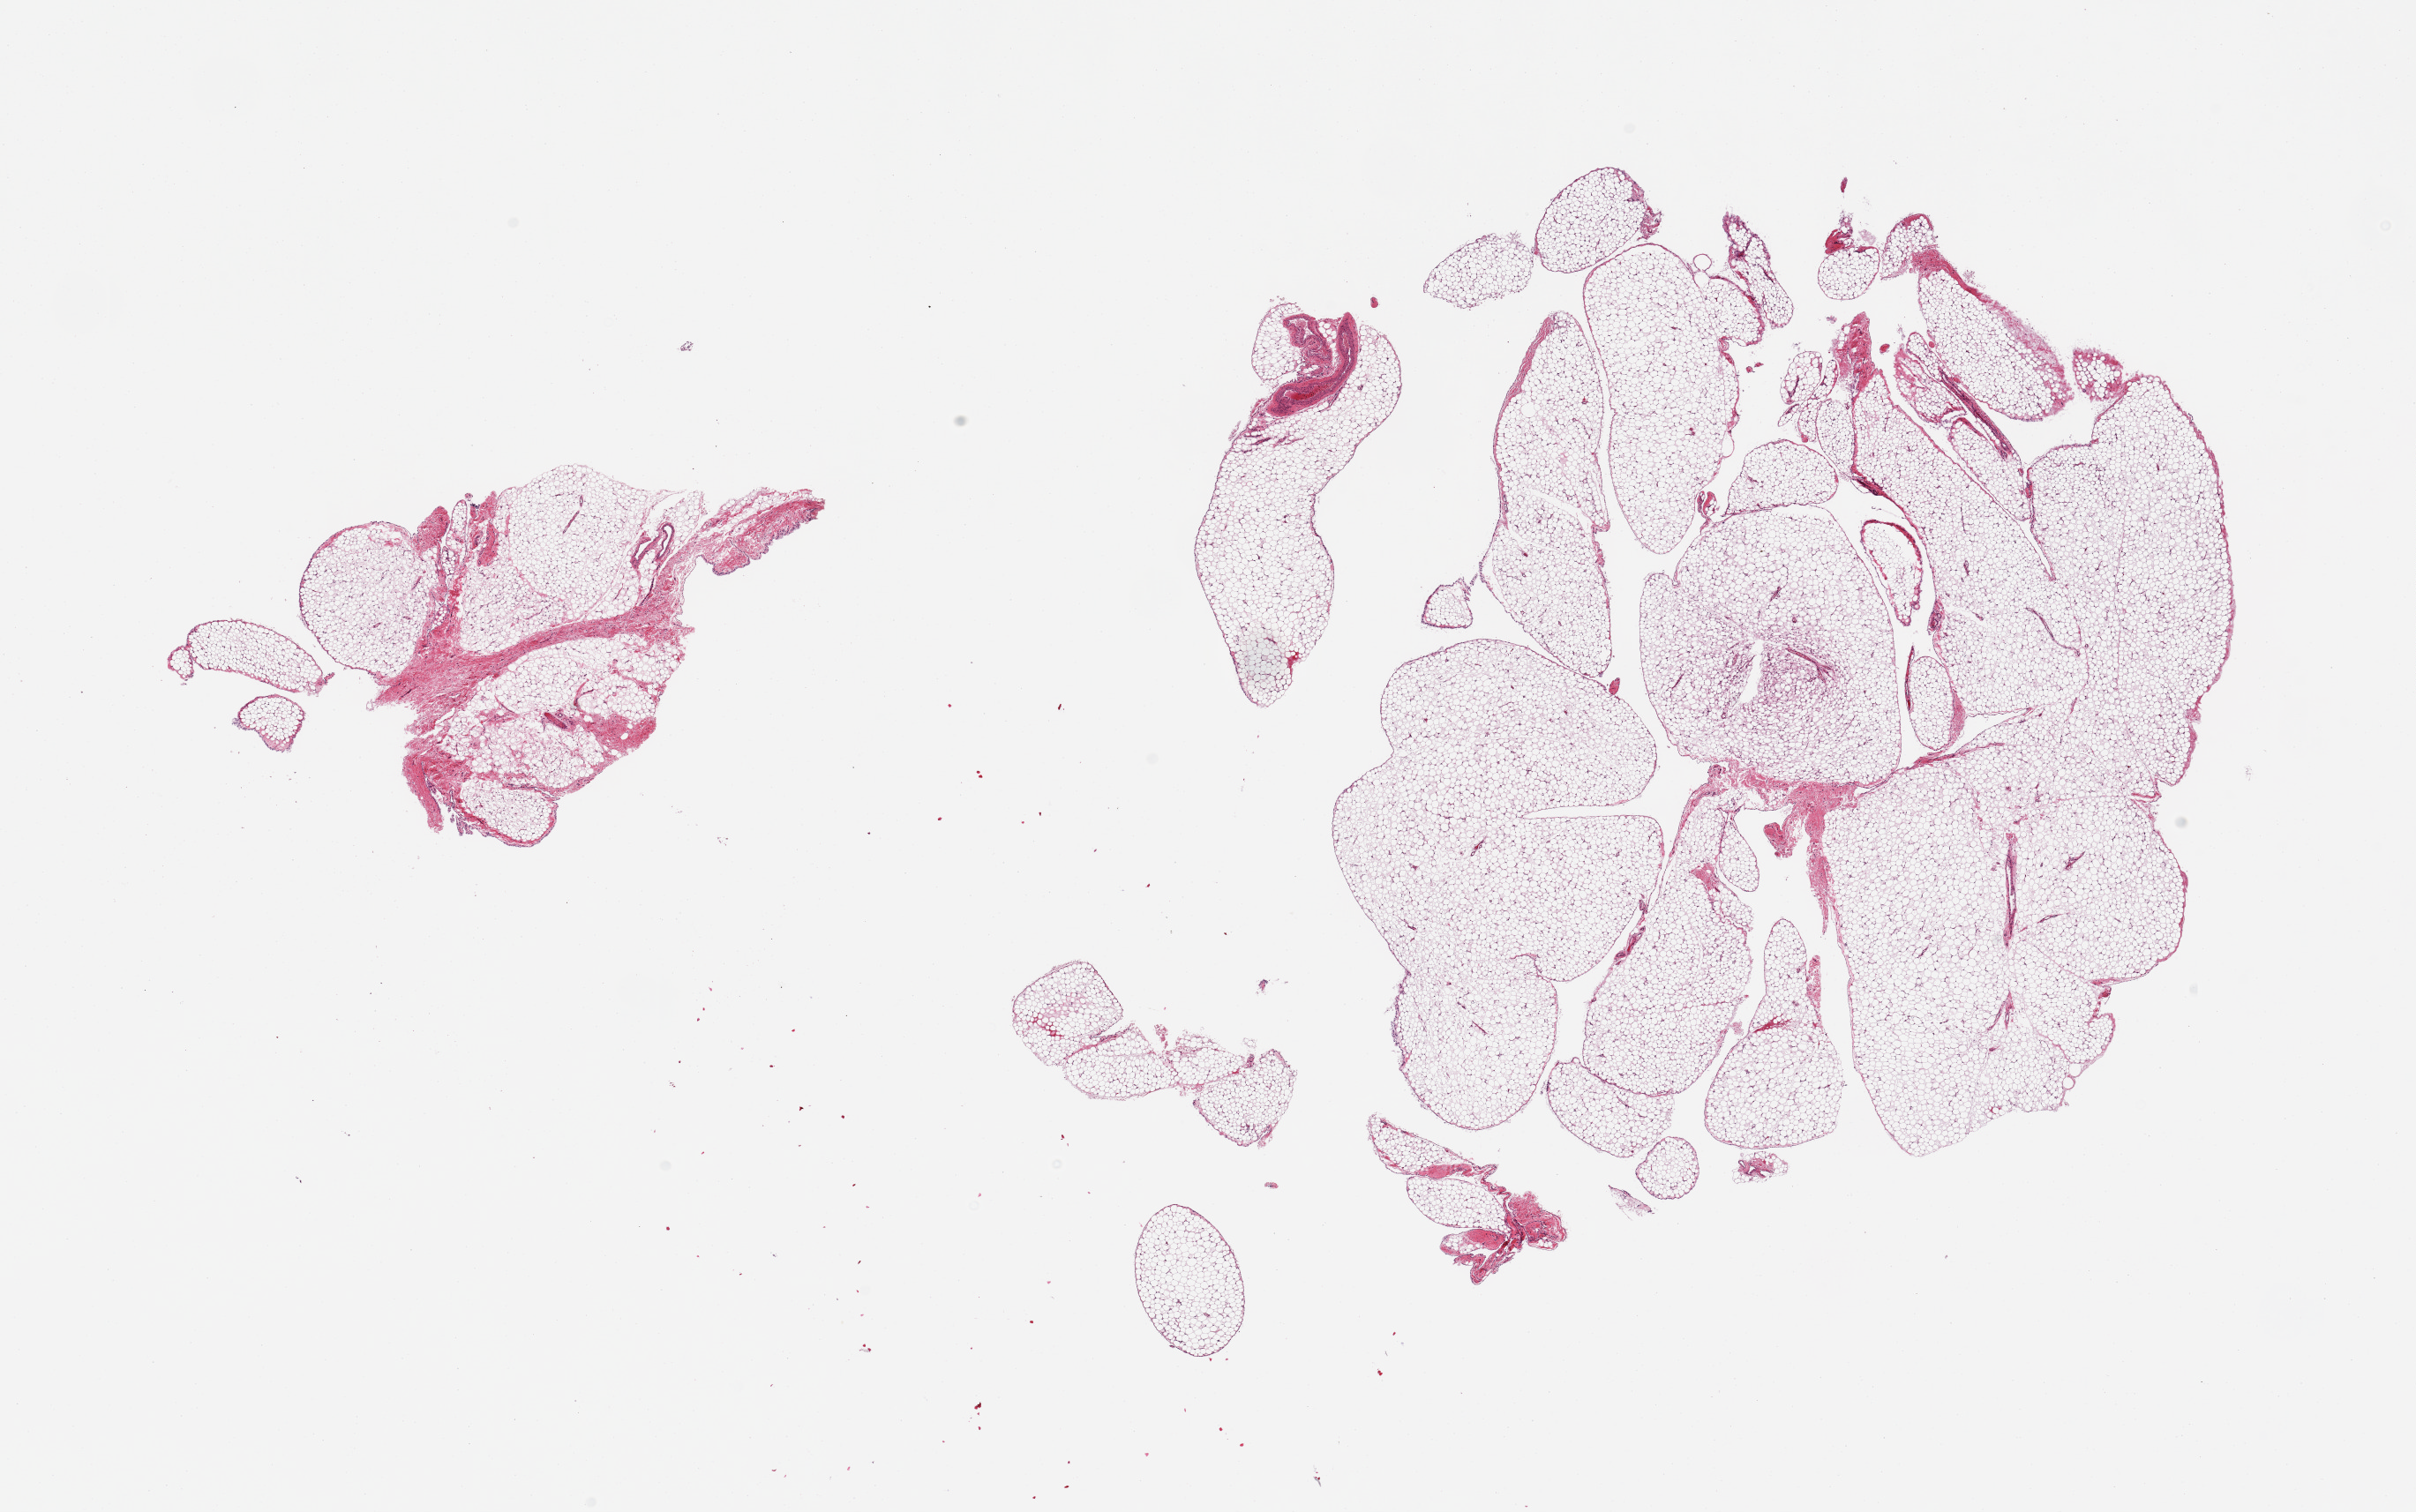
Whole-slide image, H&E stain, a low-resolution overview of the entire scanned area, about 21.7 x 13.6 mm (acquisition: 20x scan), PAXgene-fixed paraffin-embedded (PFPE) section, target tissue: omentum, donor tissue sample. Donor: female.
Review note (as recorded): 2 pieces.